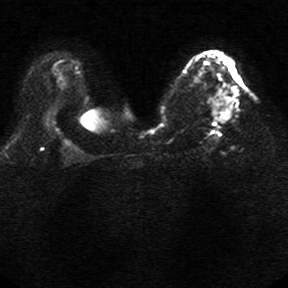
Breast MRI, one axial slice; slice 16 of 34 in the series (ordered by position); diffusion-weighted series; image 2 of 4 stored at this slice position (different b-values; order by instance number); 1.5 T; 288 × 288 image matrix, field of view 340 × 340 mm. Female patient.
Outlined on this slice (expert manual segmentation):
- tumour on diffusion-weighted imaging: bounding box (x1, y1, x2, y2) in pixels: (219, 87, 238, 122)